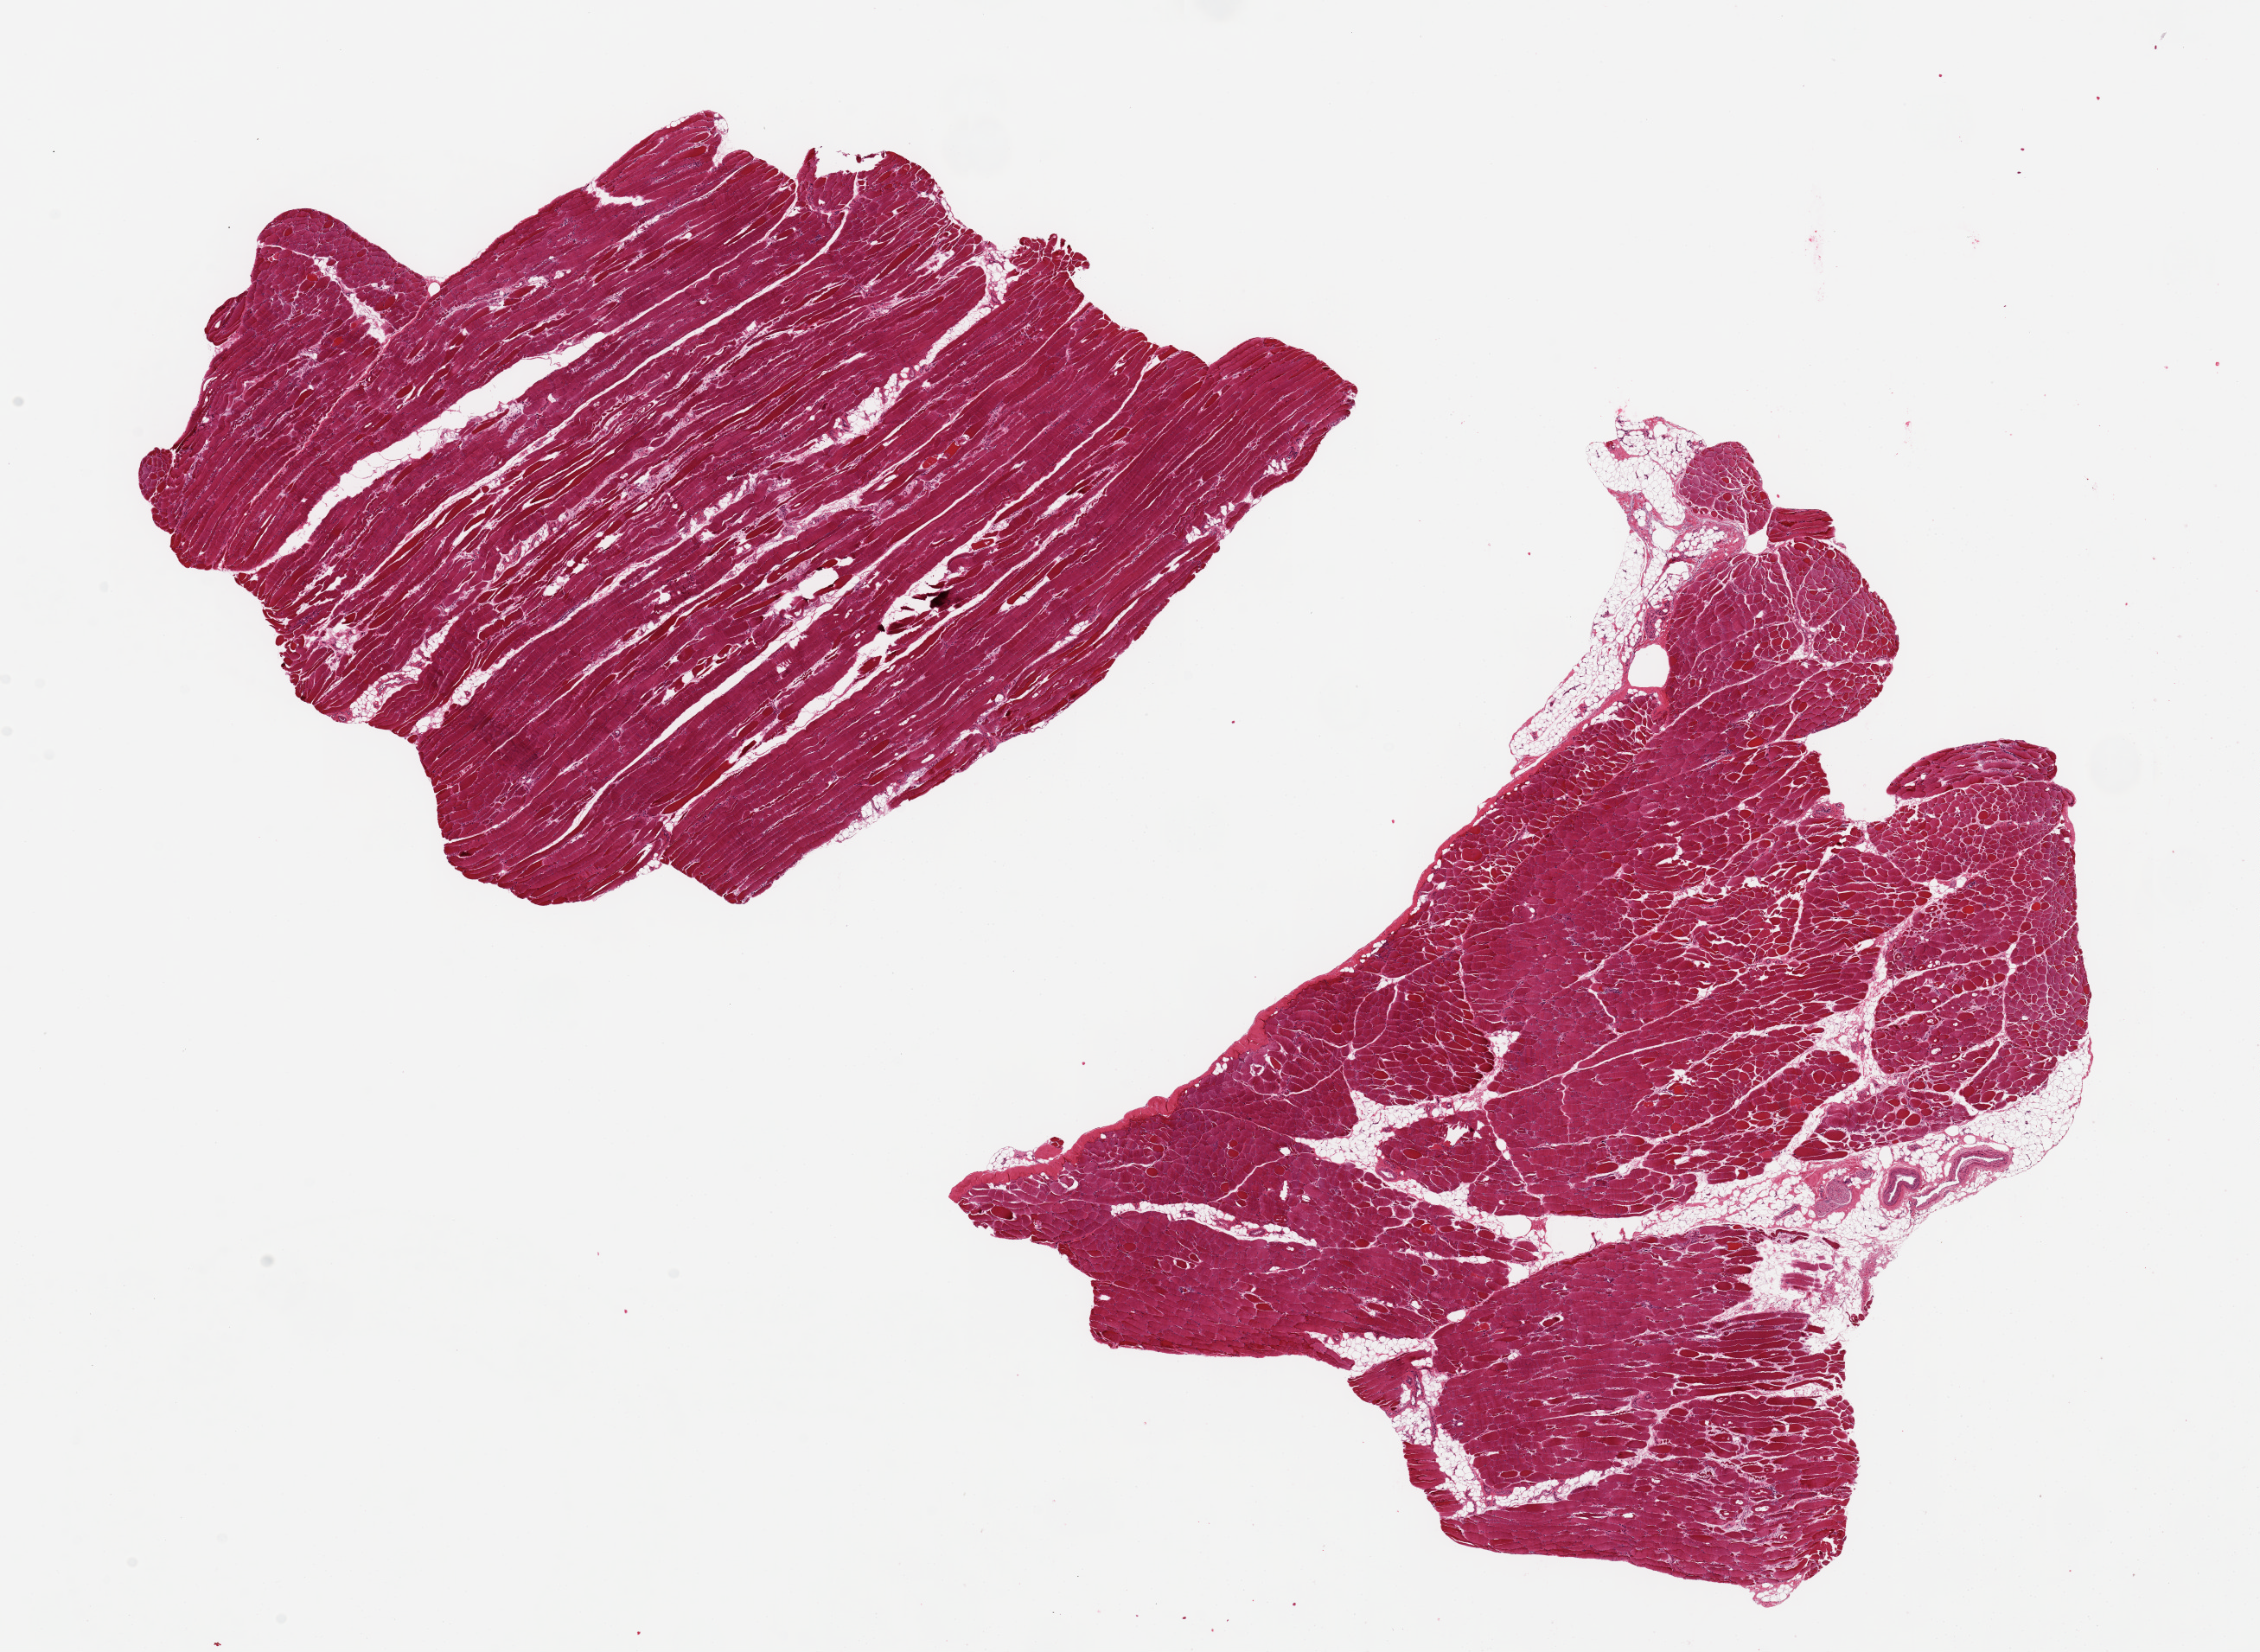
Hematoxylin and eosin (H&E) whole-slide image, brightfield — shown as a low-resolution overview of the whole scanned area (about 20.7 x 15.1 mm, acquisition: 20x scan). PAXgene-fixed paraffin-embedded (PFPE) section. Section of skeletal muscle (target tissue). Donor tissue sample. Female donor.
Reviewer comment on this tissue sample: 2 ~8x6mm pieces, ~5% interstitial fat.